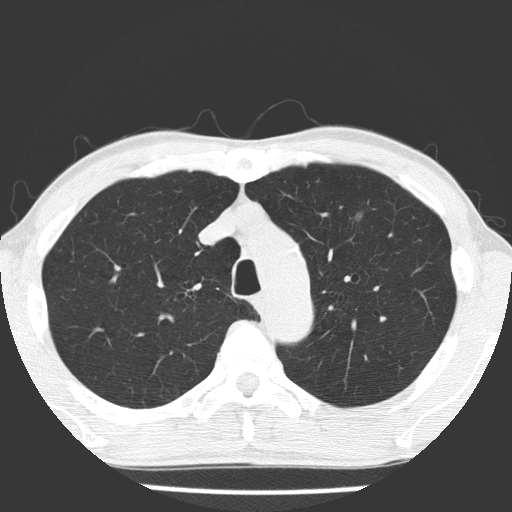
Chest CT (low-dose screening protocol), one axial image, baseline annual screen, lung window (W 1500 / L -600 HU), lung (sharp) reconstruction kernel (FC51), slice 49 of 177 in the series. Male, age 66 years at enrolment. Current smoker at enrolment.
Expert reader's lesion annotation, bounding box (x1, y1, x2, y2) in pixels: (332, 200, 382, 245). The exam's reader record, not a measurement of the box and not confirmed to be the same lesion: non-calcified nodule or mass ≥4 mm, left upper lobe, 8 × 8 mm, poorly defined margins, mixed attenuation. Official screen result: positive, change unspecified: nodule(s) >= 4 mm or enlarging nodule(s), mass(es), or other non-specific abnormalities suspicious for lung cancer.